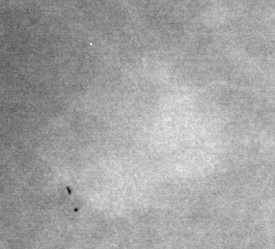
Crop from a digitized film mammogram around one marked abnormality; right breast; MLO view.
- Marked abnormality: mass, shape lobulated, margins circumscribed; BI-RADS assessment category 3; subtlety rating 5 on a 1 (subtle) to 5 (obvious) scale; pathology result (as recorded, not read from the image): benign.